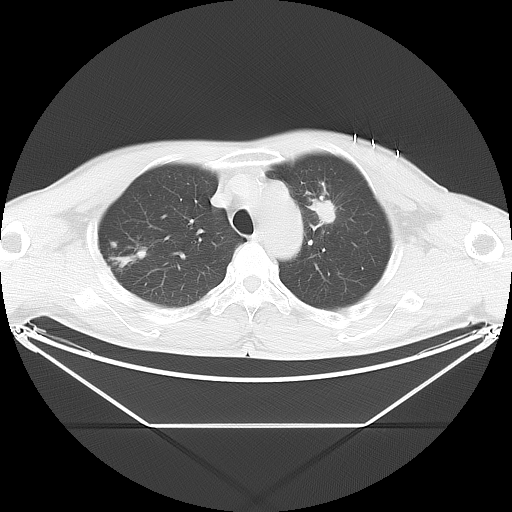
Chest CT, one axial slice. Position 21 of 28 along the scan axis. Reconstruction kernel LUNG. 120 kVp. Lung window (W 1500 / L -600 HU). 5 mm slice thickness. 512 × 512 image matrix. Male patient, age 60 years. Case-level facts recorded for this patient, not image findings: clinical TNM (as recorded): T2 N1 M0.
Structures marked on this image (rectangle marked by the reading radiologist):
- lung tumour (recorded histology: adenocarcinoma): box from (x=304, y=198) to (x=339, y=228) px